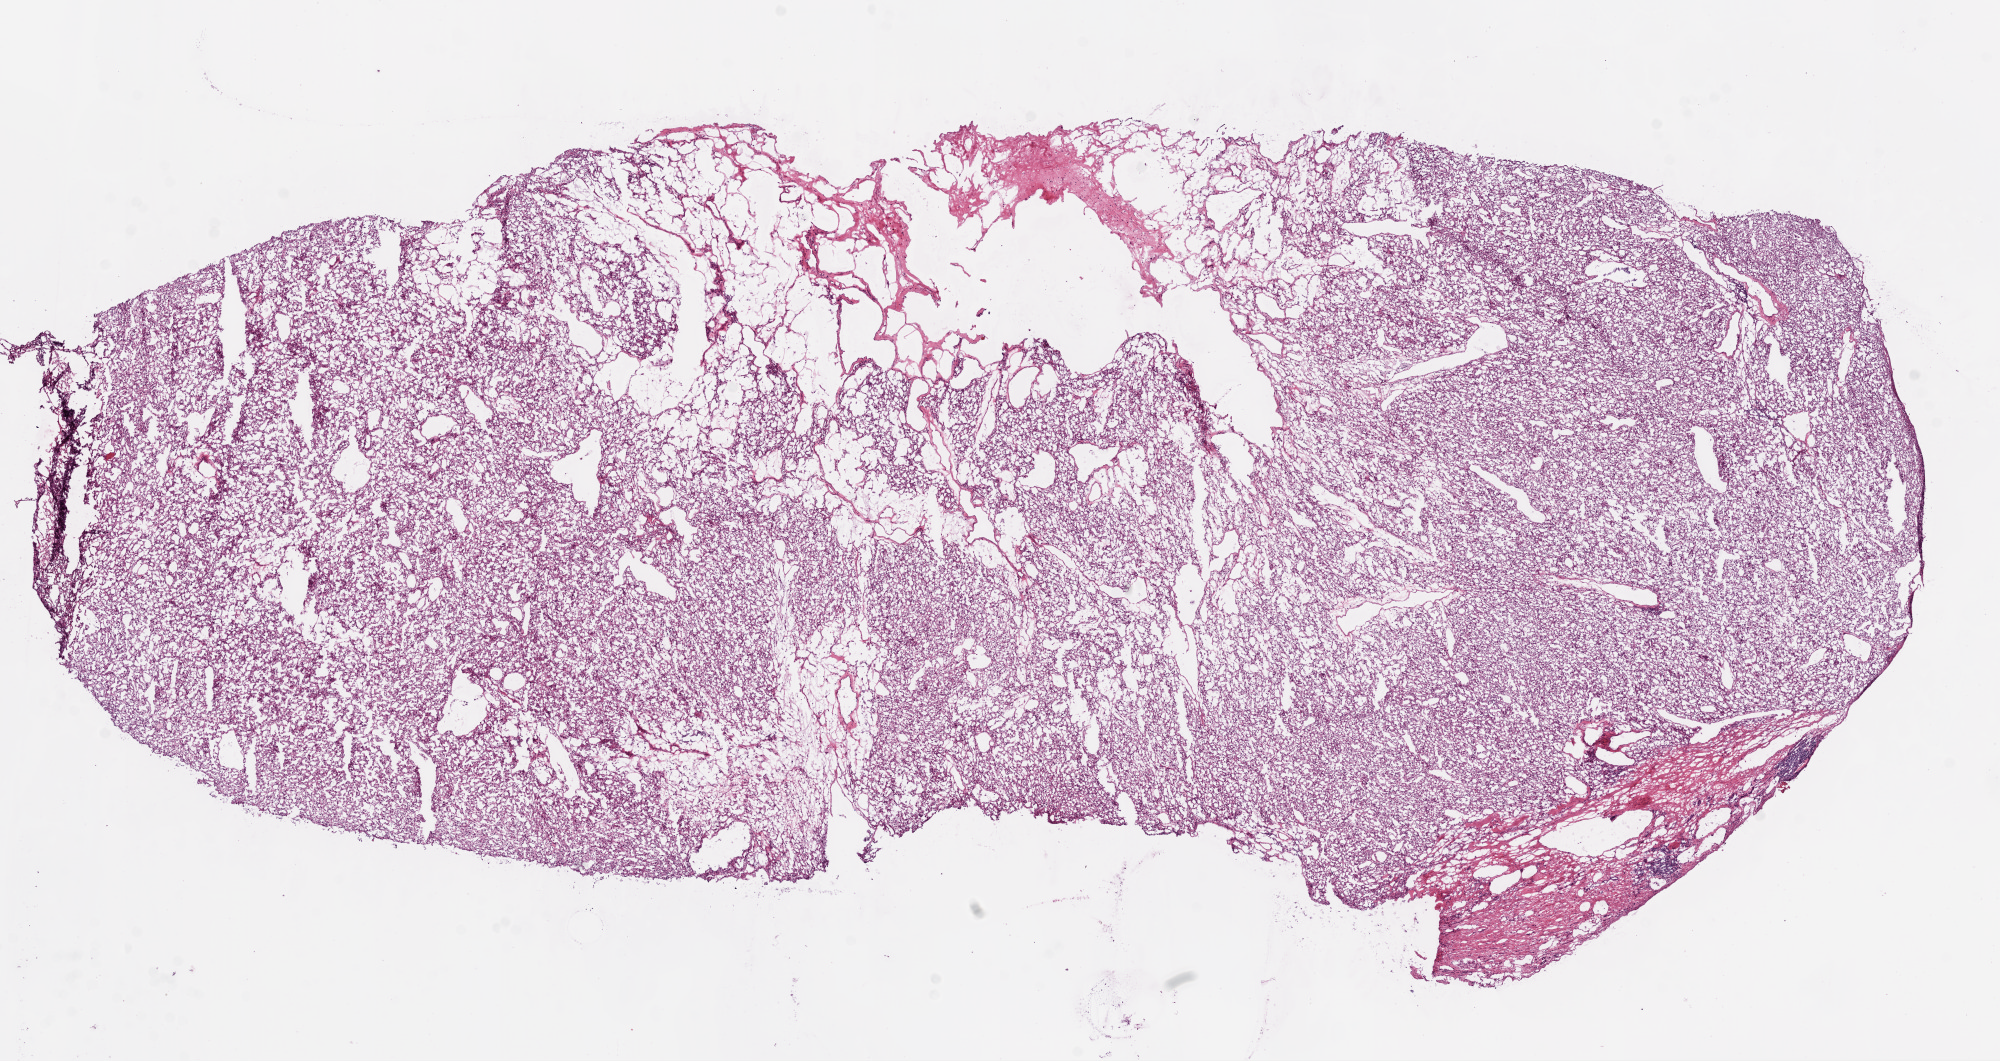
Digitized H&E-stained tissue section (whole slide) — whole scanned area (about 16.0 x 8.5 mm) shown as a low-resolution overview. Frozen section from the bottom of the tissue portion. Kidney, primary tumour sample. Patient: male, age at initial diagnosis 52 years. Histologic grade: G2 (moderately differentiated). Pathologist review of this section (percent, as recorded): tumour cells 95%, tumour nuclei 90%, stromal cells 5%, necrosis 0%. Infiltration values recorded for this section: lymphocyte infiltration 3%.
TNM: T1a NX M0. Diagnosis: Clear cell adenocarcinoma, NOS. AJCC pathologic stage: I.